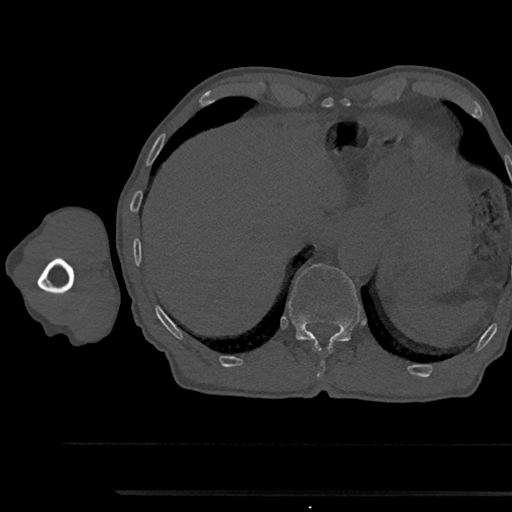
CT including the spine, one axial slice. Position 745 of 797 along the scan axis. 120 kVp. Bone window (W 1800 / L 400 HU). 512 × 512 image matrix, field of view 367 × 367 mm. Patient: male, 79 years. Case-level facts recorded for this patient, not image findings: primary cancer: prostate.
Annotated regions visible in this slice (semi-automatically segmented with operator editing):
- T11 vertebra: bounding box (x1, y1, x2, y2) in pixels: (314, 342, 333, 376)
- T12 vertebra: (287, 264, 360, 344)